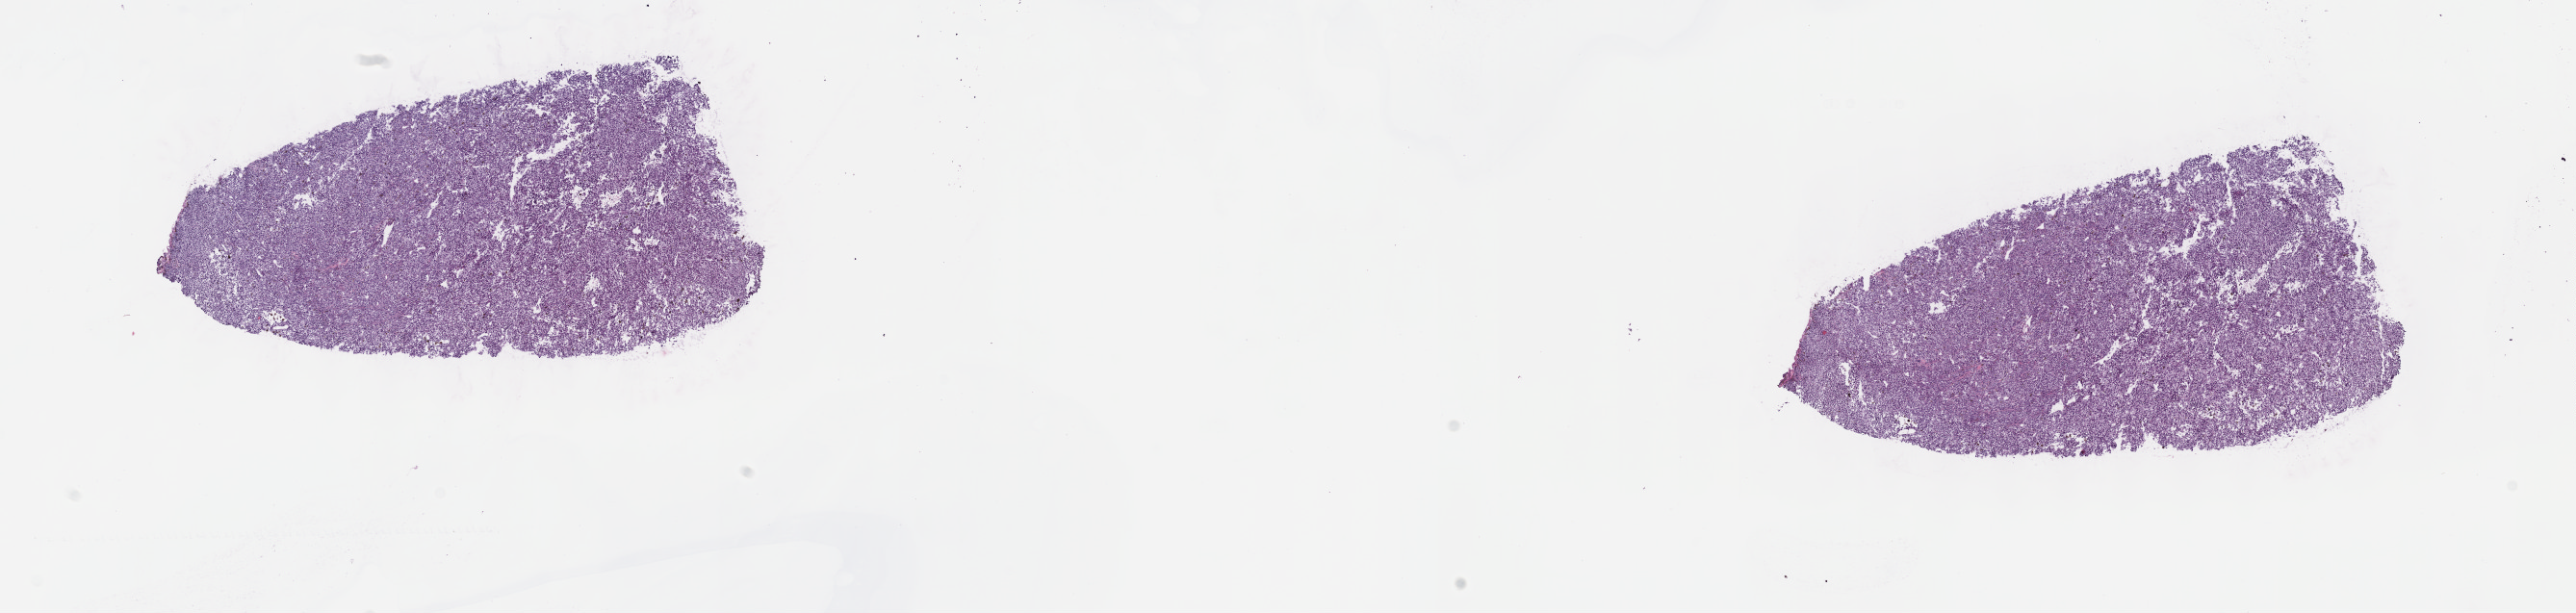
Digitized H&E tissue section (whole slide) — a low-resolution overview of the entire scanned area, about 21.6 x 5.2 mm (slide scanned at 40x). Frozen section from the top of the tissue portion. Sample: primary tumour, uvea. Patient: female, age at initial diagnosis 47 years. Composition of this section per pathologist review: tumour cells 100%, tumour nuclei 80%, normal cells 0%, stromal cells 0%, necrosis 0%. Infiltration values recorded for this section: lymphocyte infiltration 1%, monocyte infiltration 0%, neutrophil infiltration 0%.
TNM: T2a NX MX. AJCC pathologic stage: IIA (7th edition). Laterality: right. Histologic diagnosis: Spindle cell melanoma, type B (choroid).